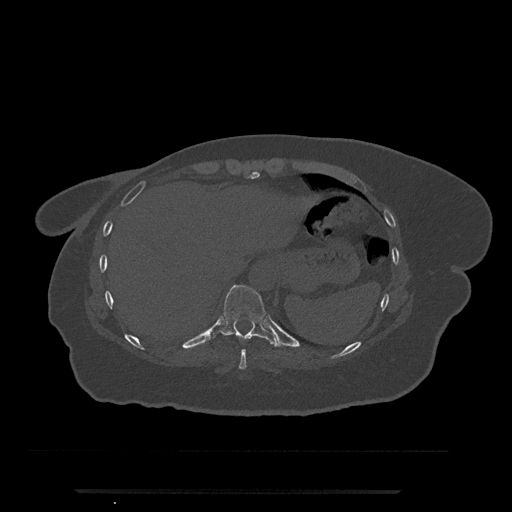
CT including the spine, one axial slice. Slice 302 of 797 in the series (ordered by position). Bone window (W 1800 / L 400 HU). 512 × 512 image matrix, field of view 440 × 440 mm. Patient: female, 51 years. Case-level facts recorded for this patient, not image findings: primary cancer: neuro.
Structures marked on this image (semi-automatically segmented with operator editing):
- T10 vertebra: bounding box <221,285,278,347> (left, top, right, bottom; pixels)
- T9 vertebra: <239,349,247,370>